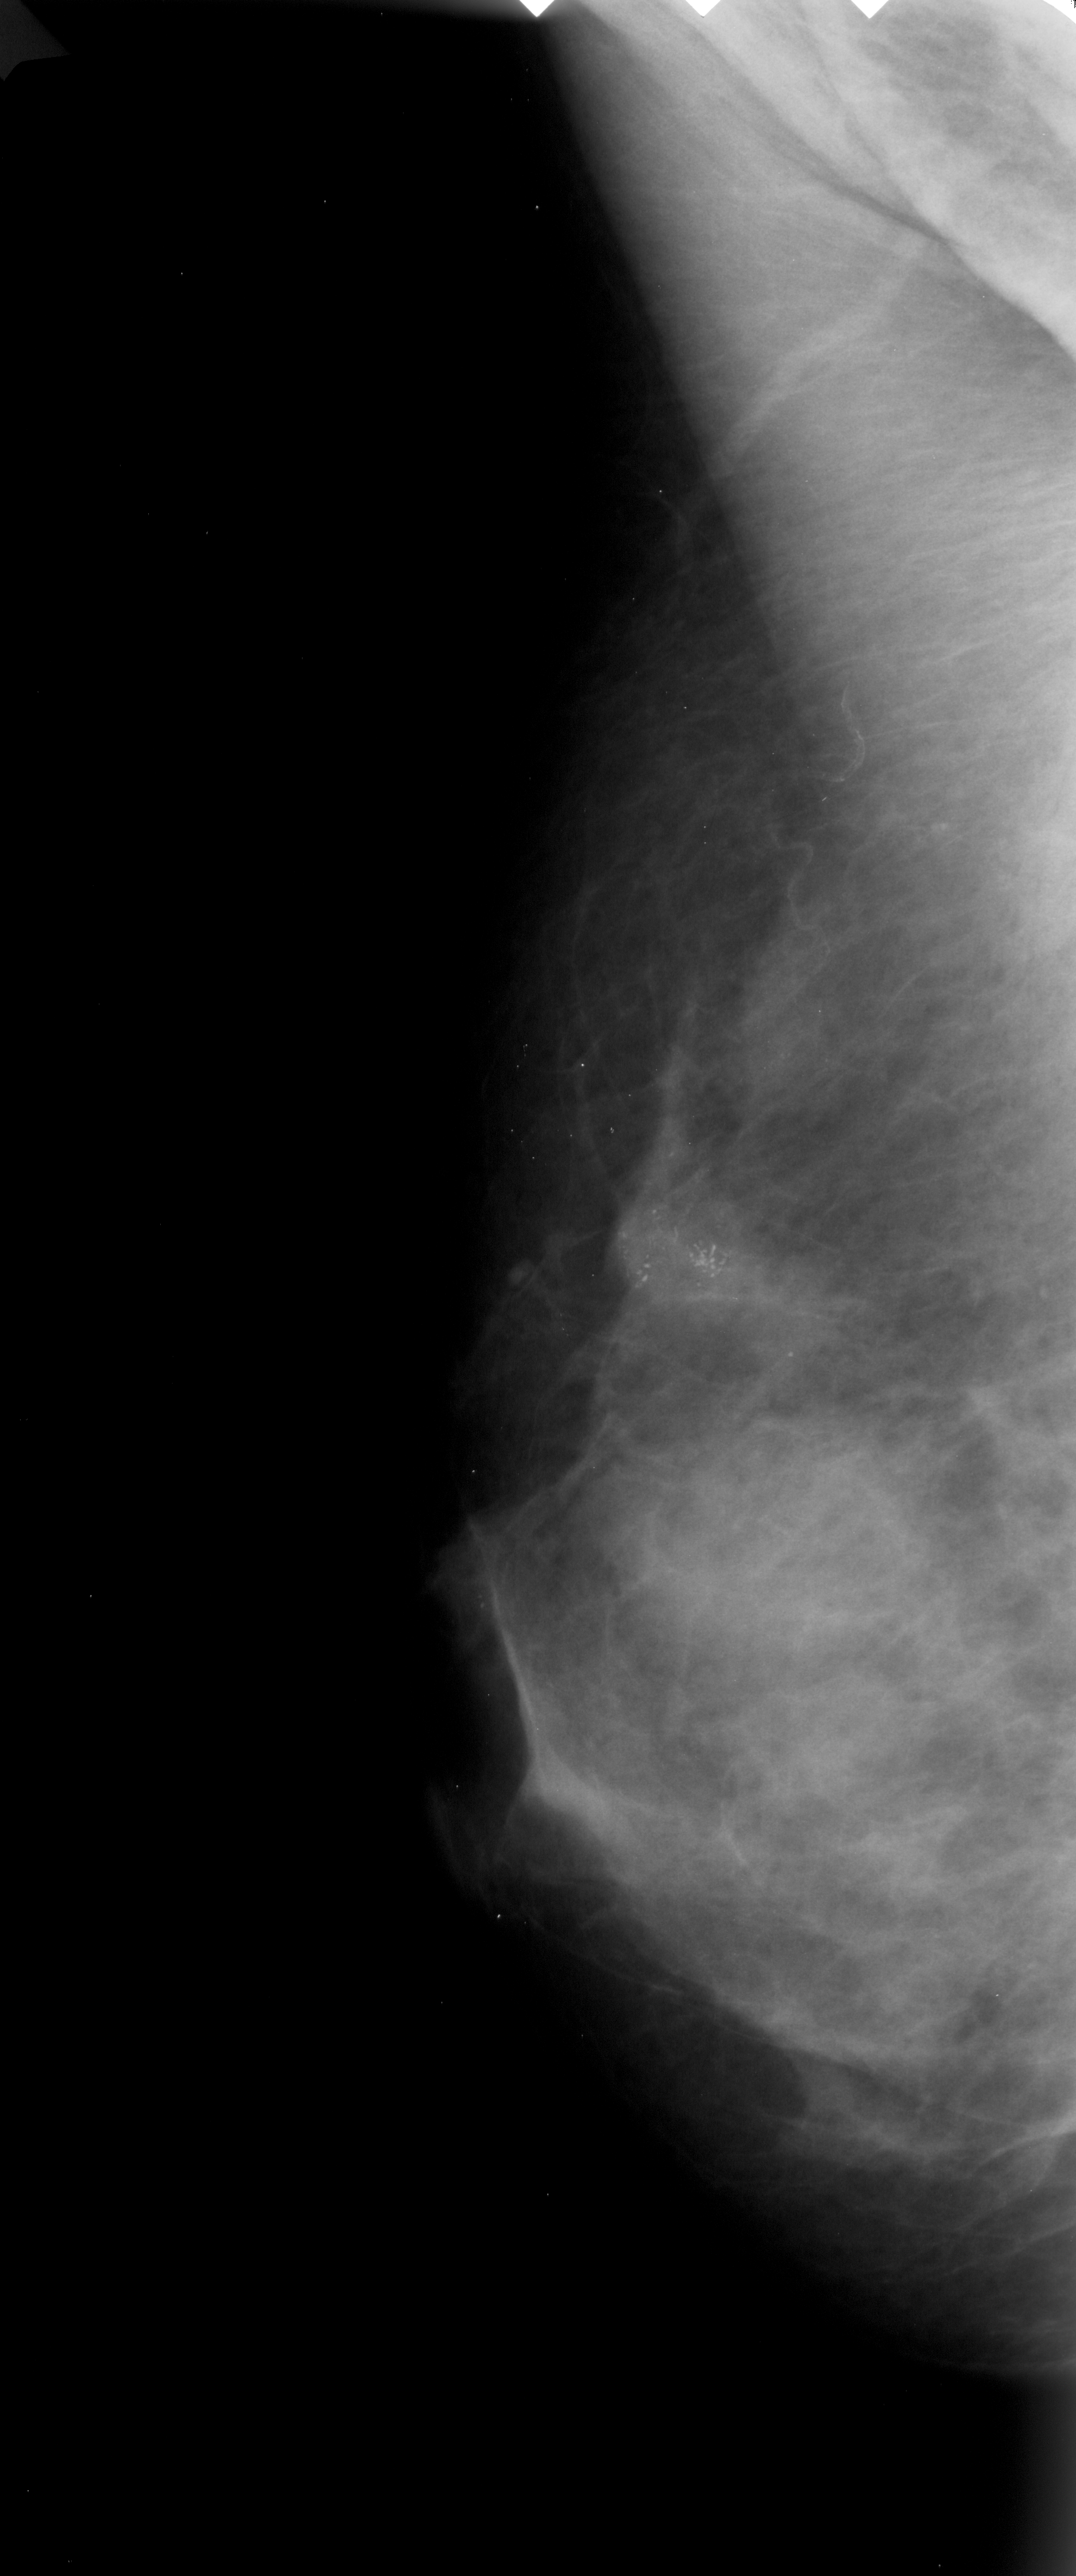
Scanned film-screen mammogram. Left breast. Mediolateral oblique (MLO) view. BI-RADS breast density category 4 (scale 1–4). 1076 × 2576 image matrix.
Expert-marked regions of interest on this image (one box per marked abnormality):
- calcifications, morphology pleomorphic, distribution clustered; BI-RADS assessment category 4; subtlety rating 5 on a 1 (subtle) to 5 (obvious) scale; pathology result (as recorded, not read from the image): malignant: bounding box (x1, y1, x2, y2) in pixels: (598, 1106, 746, 1306)